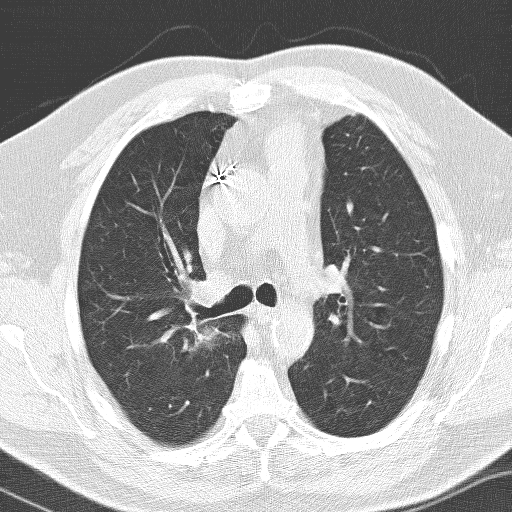
Low-dose screening chest CT, axial slice; baseline screening round; lung window (W 1500 / L -600 HU); slice 43 of 141 in the series. Male, age 66 years at enrolment. Former smoker at enrolment.
• Expert-annotated lung lesion, bounding box (x1, y1, x2, y2) in pixels: (144, 289, 233, 390).
• Reader record for this screening exam (exam-level; its link to the box is not recorded): non-calcified nodule or mass ≥4 mm, right upper lobe, 36 × 30 mm, spiculated (stellate) margins, soft tissue attenuation.